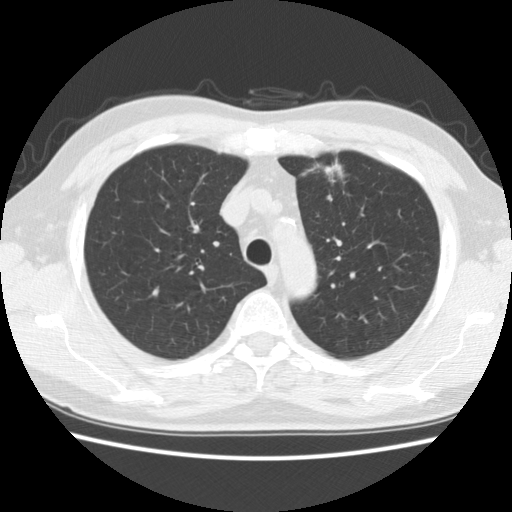
Low-dose screening chest CT, one axial slice; position 130 of 172 along the scan axis; reconstruction kernel STANDARD; lung window (W 1500 / L -600 HU); 512 × 512 image matrix, field of view 337 × 337 mm.
Outlined on this slice (outlined manually by an expert reader):
- lesion 1 (tumor, upper lobe of left lung): box from (x=324, y=164) to (x=344, y=183) px